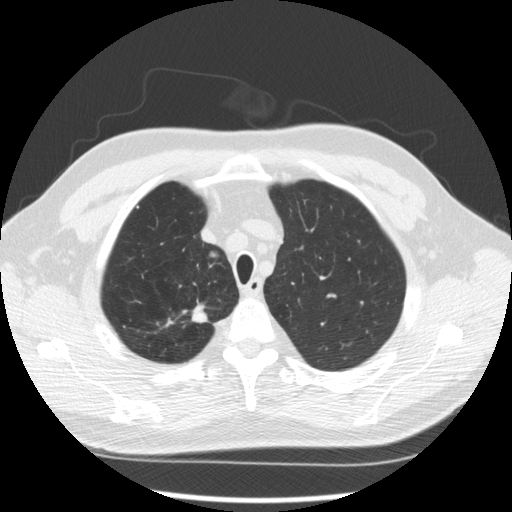
Axial slice from a low-dose chest CT screening exam; second screening round (one year after baseline); lung window (W 1500 / L -600 HU); slice 47 of 289 in the series; 512 × 512 image matrix. Male participant, aged 64 years at enrolment.
2 expert reader's lesion annotations on this slice (largest first), box from (x=170, y=298) to (x=218, y=333) px; (x=187, y=244)–(x=226, y=272). The screening reader recorded 3 non-calcified nodules or masses ≥4 mm on this exam (right upper lobe, right upper lobe, right upper lobe); which of them these boxes mark is not recorded. Official screen result: positive, other. Later outcome: lung cancer diagnosed 411 days after this screen — adenocarcinoma, NOS, right upper lobe, moderately differentiated (G2), stage IA (AJCC 6th edition), 14 mm at pathology.